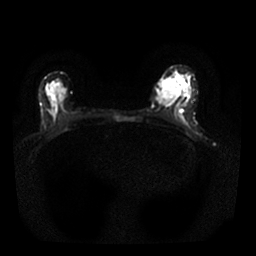
Breast MRI, one axial slice. Slice 11 of 25 in the series (ordered by position). Diffusion-weighted series; image 2 of 4 stored at this slice position (different b-values; order by instance number). 1.5 T. 4 mm slice thickness. 256 × 256 image matrix, field of view 310 × 310 mm. Female patient.
Annotated regions visible in this slice (expert manual segmentation):
- tumour on diffusion-weighted imaging: bounding box (x1, y1, x2, y2) in pixels: (157, 80, 179, 106)